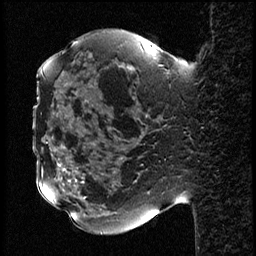
Breast MRI (dynamic contrast-enhanced), one sagittal slice; position 22 of 78 along the scan axis; dynamic contrast-enhanced study with each time point stored as its own series, time point 2 of 3 at this slice position (early post-contrast, ordered by acquisition time); 1.5 T; TE 4.2 ms, TR 17.6 ms; 2 mm slice thickness; 256 × 256 image matrix, field of view 200 × 200 mm. Female patient, age 42 years. Case-level facts recorded for this patient, not image findings: setting: breast cancer imaged before/during neoadjuvant chemotherapy; receptor status: HER2-positive.
Outlined on this slice (semi-automatically segmented with operator editing):
- analysis volume of interest (the breast-tissue region the enhancement analysis was run in; not a lesion): bounding box [x1, y1, x2, y2] px = [50, 48, 131, 129]
- tumour enhancement mask (voxels above the 100 % enhancement threshold inside the analysis volume of interest): [128, 66, 131, 69]